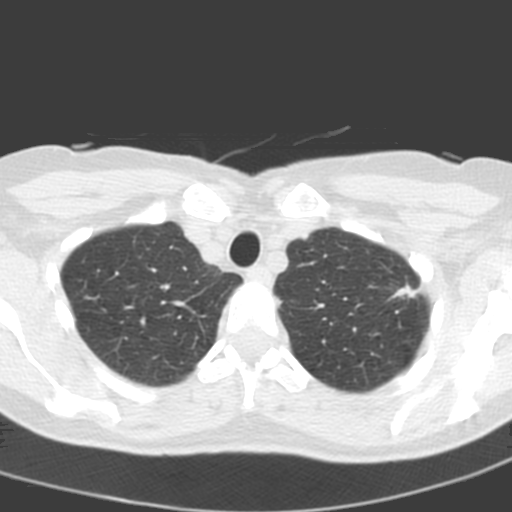
Low-dose screening chest CT, one axial slice; position 163 of 193 along the scan axis; 120 kVp; lung window (W 1500 / L -600 HU); 3.2 mm slice thickness; 512 × 512 image matrix, field of view 272 × 272 mm.
Annotated regions visible in this slice (outlined manually by an expert reader):
- lesion 1 (tumor, upper lobe of left lung): bounding box [x1, y1, x2, y2] px = [393, 285, 417, 298]